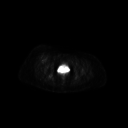
FDG PET of an extremity soft-tissue mass (from a PET/CT study), one axial slice; slice 68 of 267 in the series (ordered by position); 128 × 128 image matrix, field of view 700 × 700 mm. Female patient, age 56 years. From the clinical record (not read from this slice): histological type: malignant solitary fibrous tumor; grade: intermediate; site of the primary tumour: right thigh.
Annotated regions visible in this slice (expert contour drawn on MRI and transferred to this co-registered scan by the dataset authors):
- gross tumour volume including surrounding oedema: bounding box (x1, y1, x2, y2) in pixels: (37, 56, 48, 62)